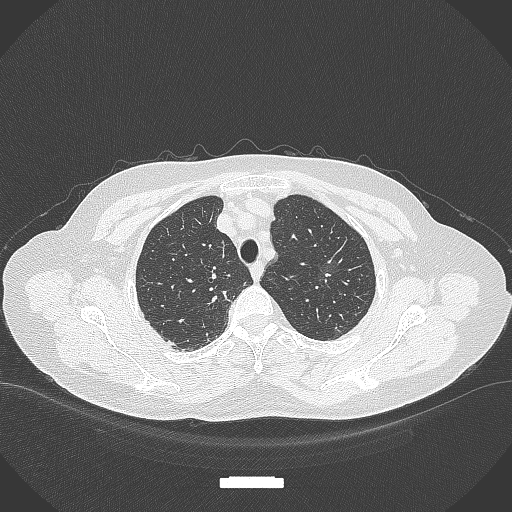
Chest CT, one axial slice; position 295 of 369 along the scan axis; reconstruction kernel B70f; 120 kVp; lung window (W 1500 / L -600 HU); 1 mm slice thickness; 512 × 512 image matrix. Female patient, age 64 years. Case-level facts recorded for this patient, not image findings: clinical TNM (as recorded): T1c N0 M0; histopathological grade: G1.
Outlined on this slice (bounding box drawn by a radiologist):
- lung tumour (recorded histology: adenocarcinoma): box from (x=308, y=255) to (x=345, y=285) px